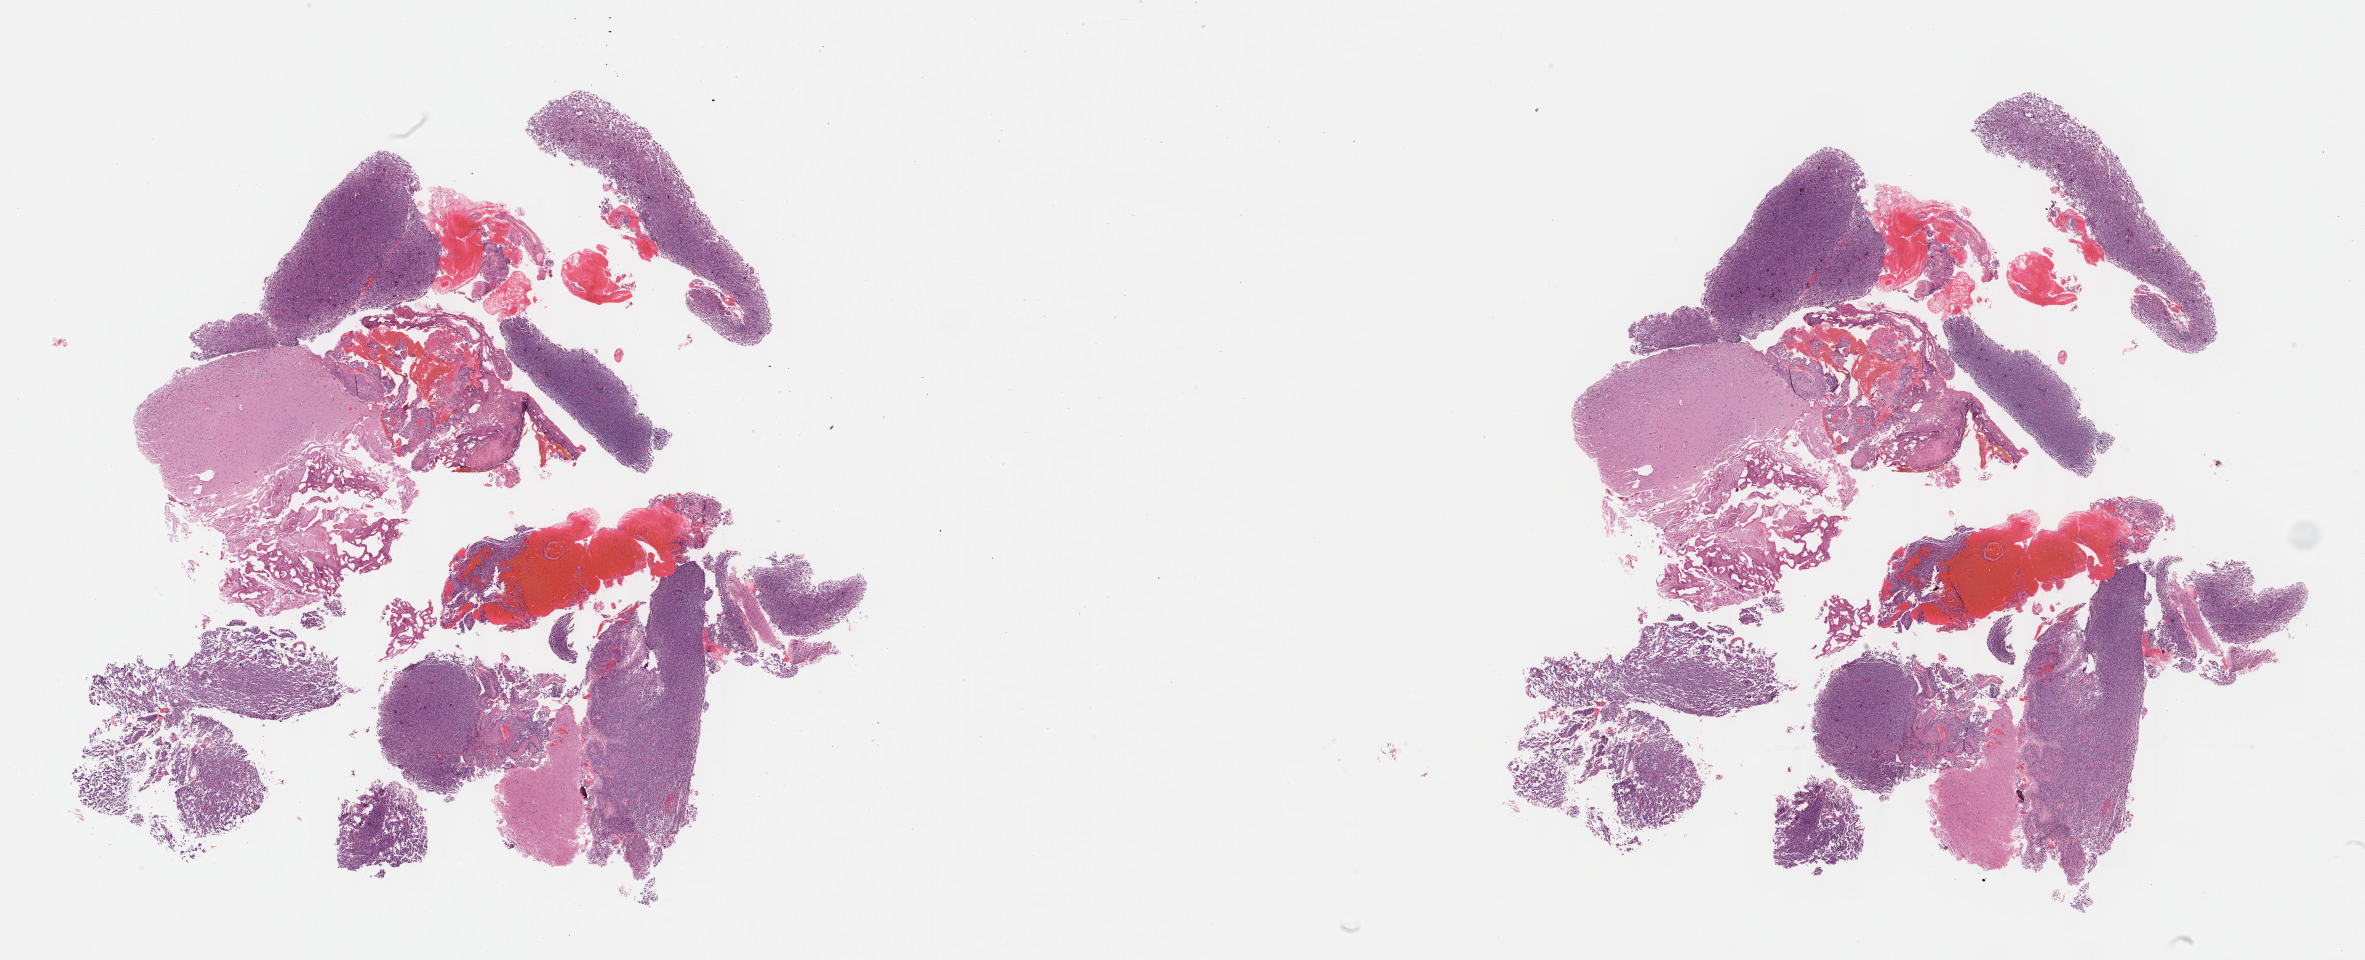
H&E-stained whole-slide image — a low-resolution overview of the entire scanned area, about 38.2 x 15.5 mm, formalin-fixed paraffin-embedded (FFPE) diagnostic section, primary tumour sample from the brain. Female, age 31 years at initial diagnosis.
- histologic diagnosis: Glioblastoma